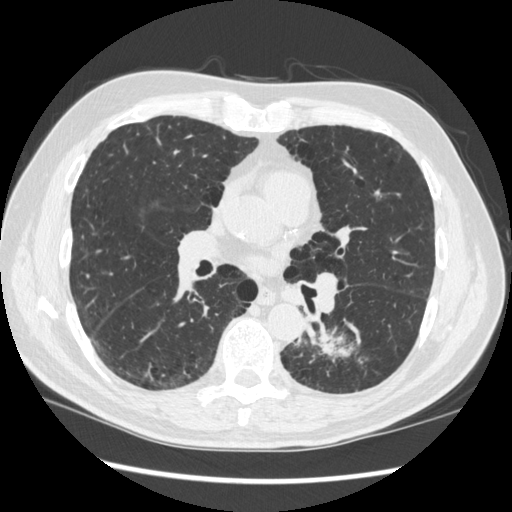
Axial slice from a low-dose chest CT screening exam, baseline annual screen, lung window (W 1500 / L -600 HU), 1.25 mm slice thickness, slice 168 of 348 in the series. Male participant, aged 72 years at enrolment.
Lesion marked by an expert reader, bounding box (x1, y1, x2, y2) in pixels: (264, 307, 368, 400). The screening reader recorded 2 non-calcified nodules or masses ≥4 mm on this exam; which of them this box marks is not recorded. Official screen result: positive, change unspecified: nodule(s) >= 4 mm or enlarging nodule(s), mass(es), or other non-specific abnormalities suspicious for lung cancer. Participant outcome: lung cancer diagnosed 37 days after this screen — squamous cell carcinoma, NOS, left lower lobe, stage IIIA (AJCC 6th edition), 60 mm at pathology.